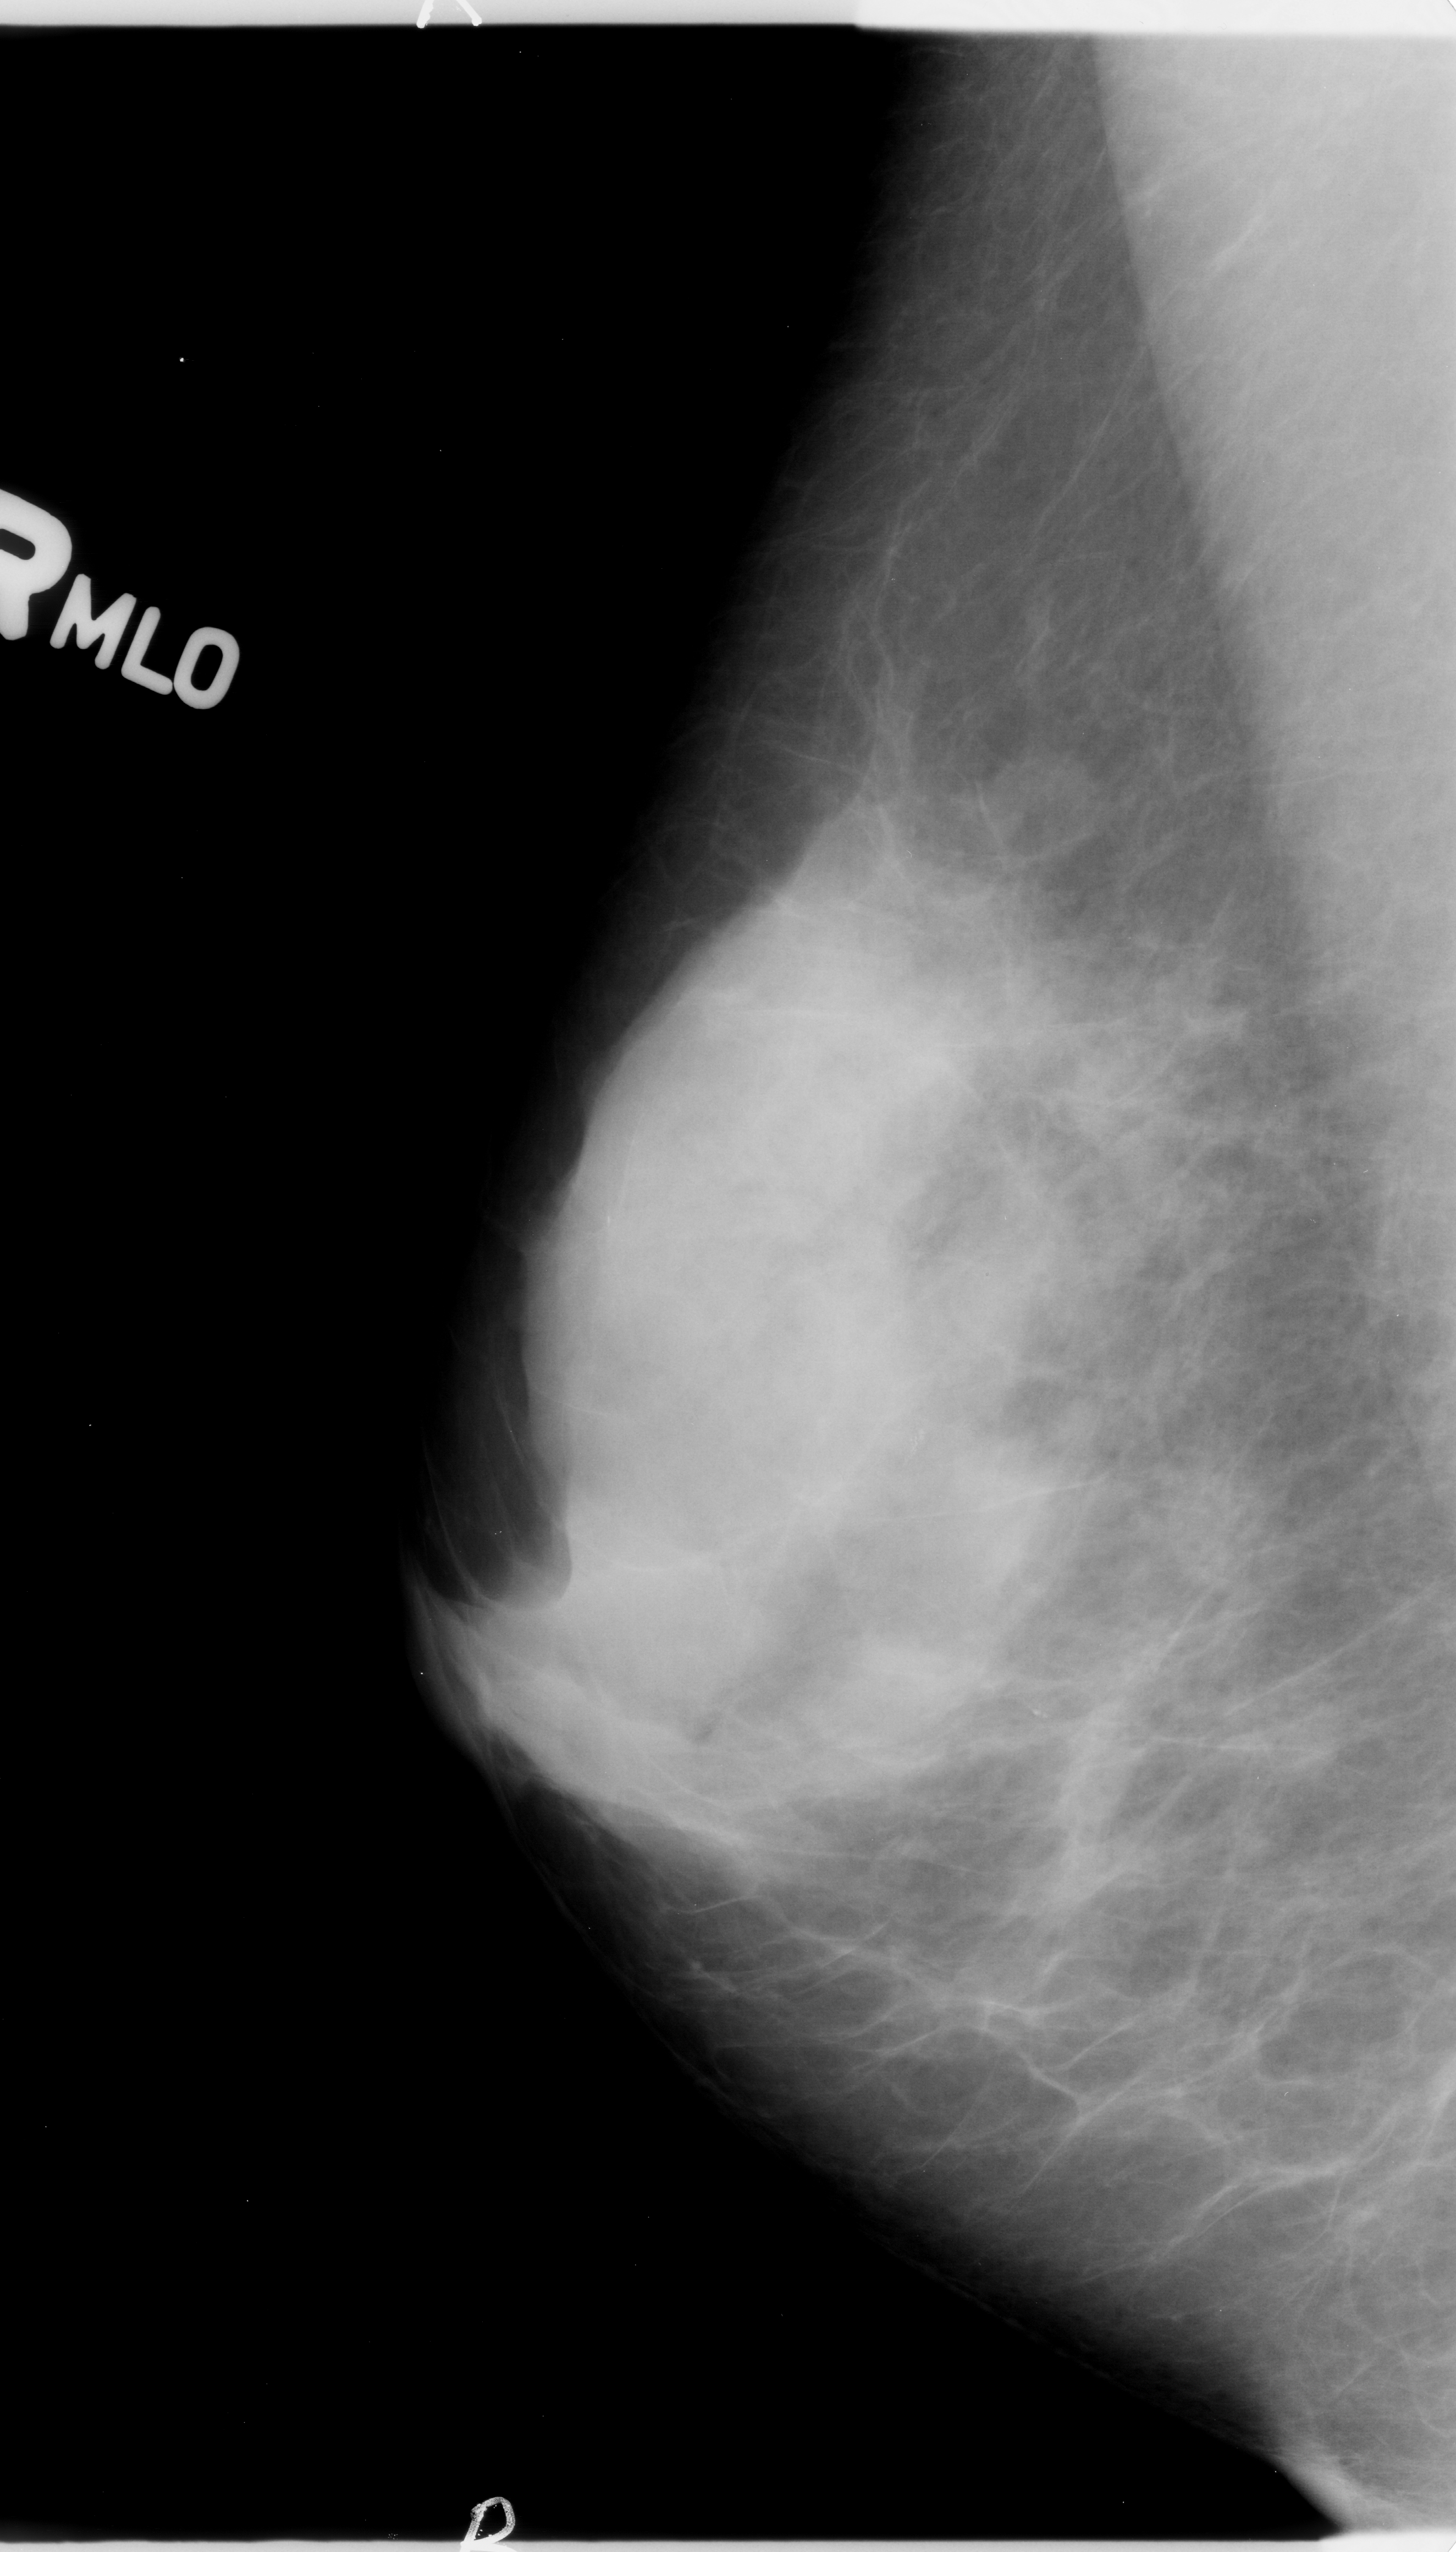
Scanned film-screen mammogram; right breast; MLO view; BI-RADS breast density category 4 (scale 1–4).
Marked abnormality: calcifications, morphology pleomorphic, distribution clustered; BI-RADS assessment category 4; pathology (as recorded): benign.